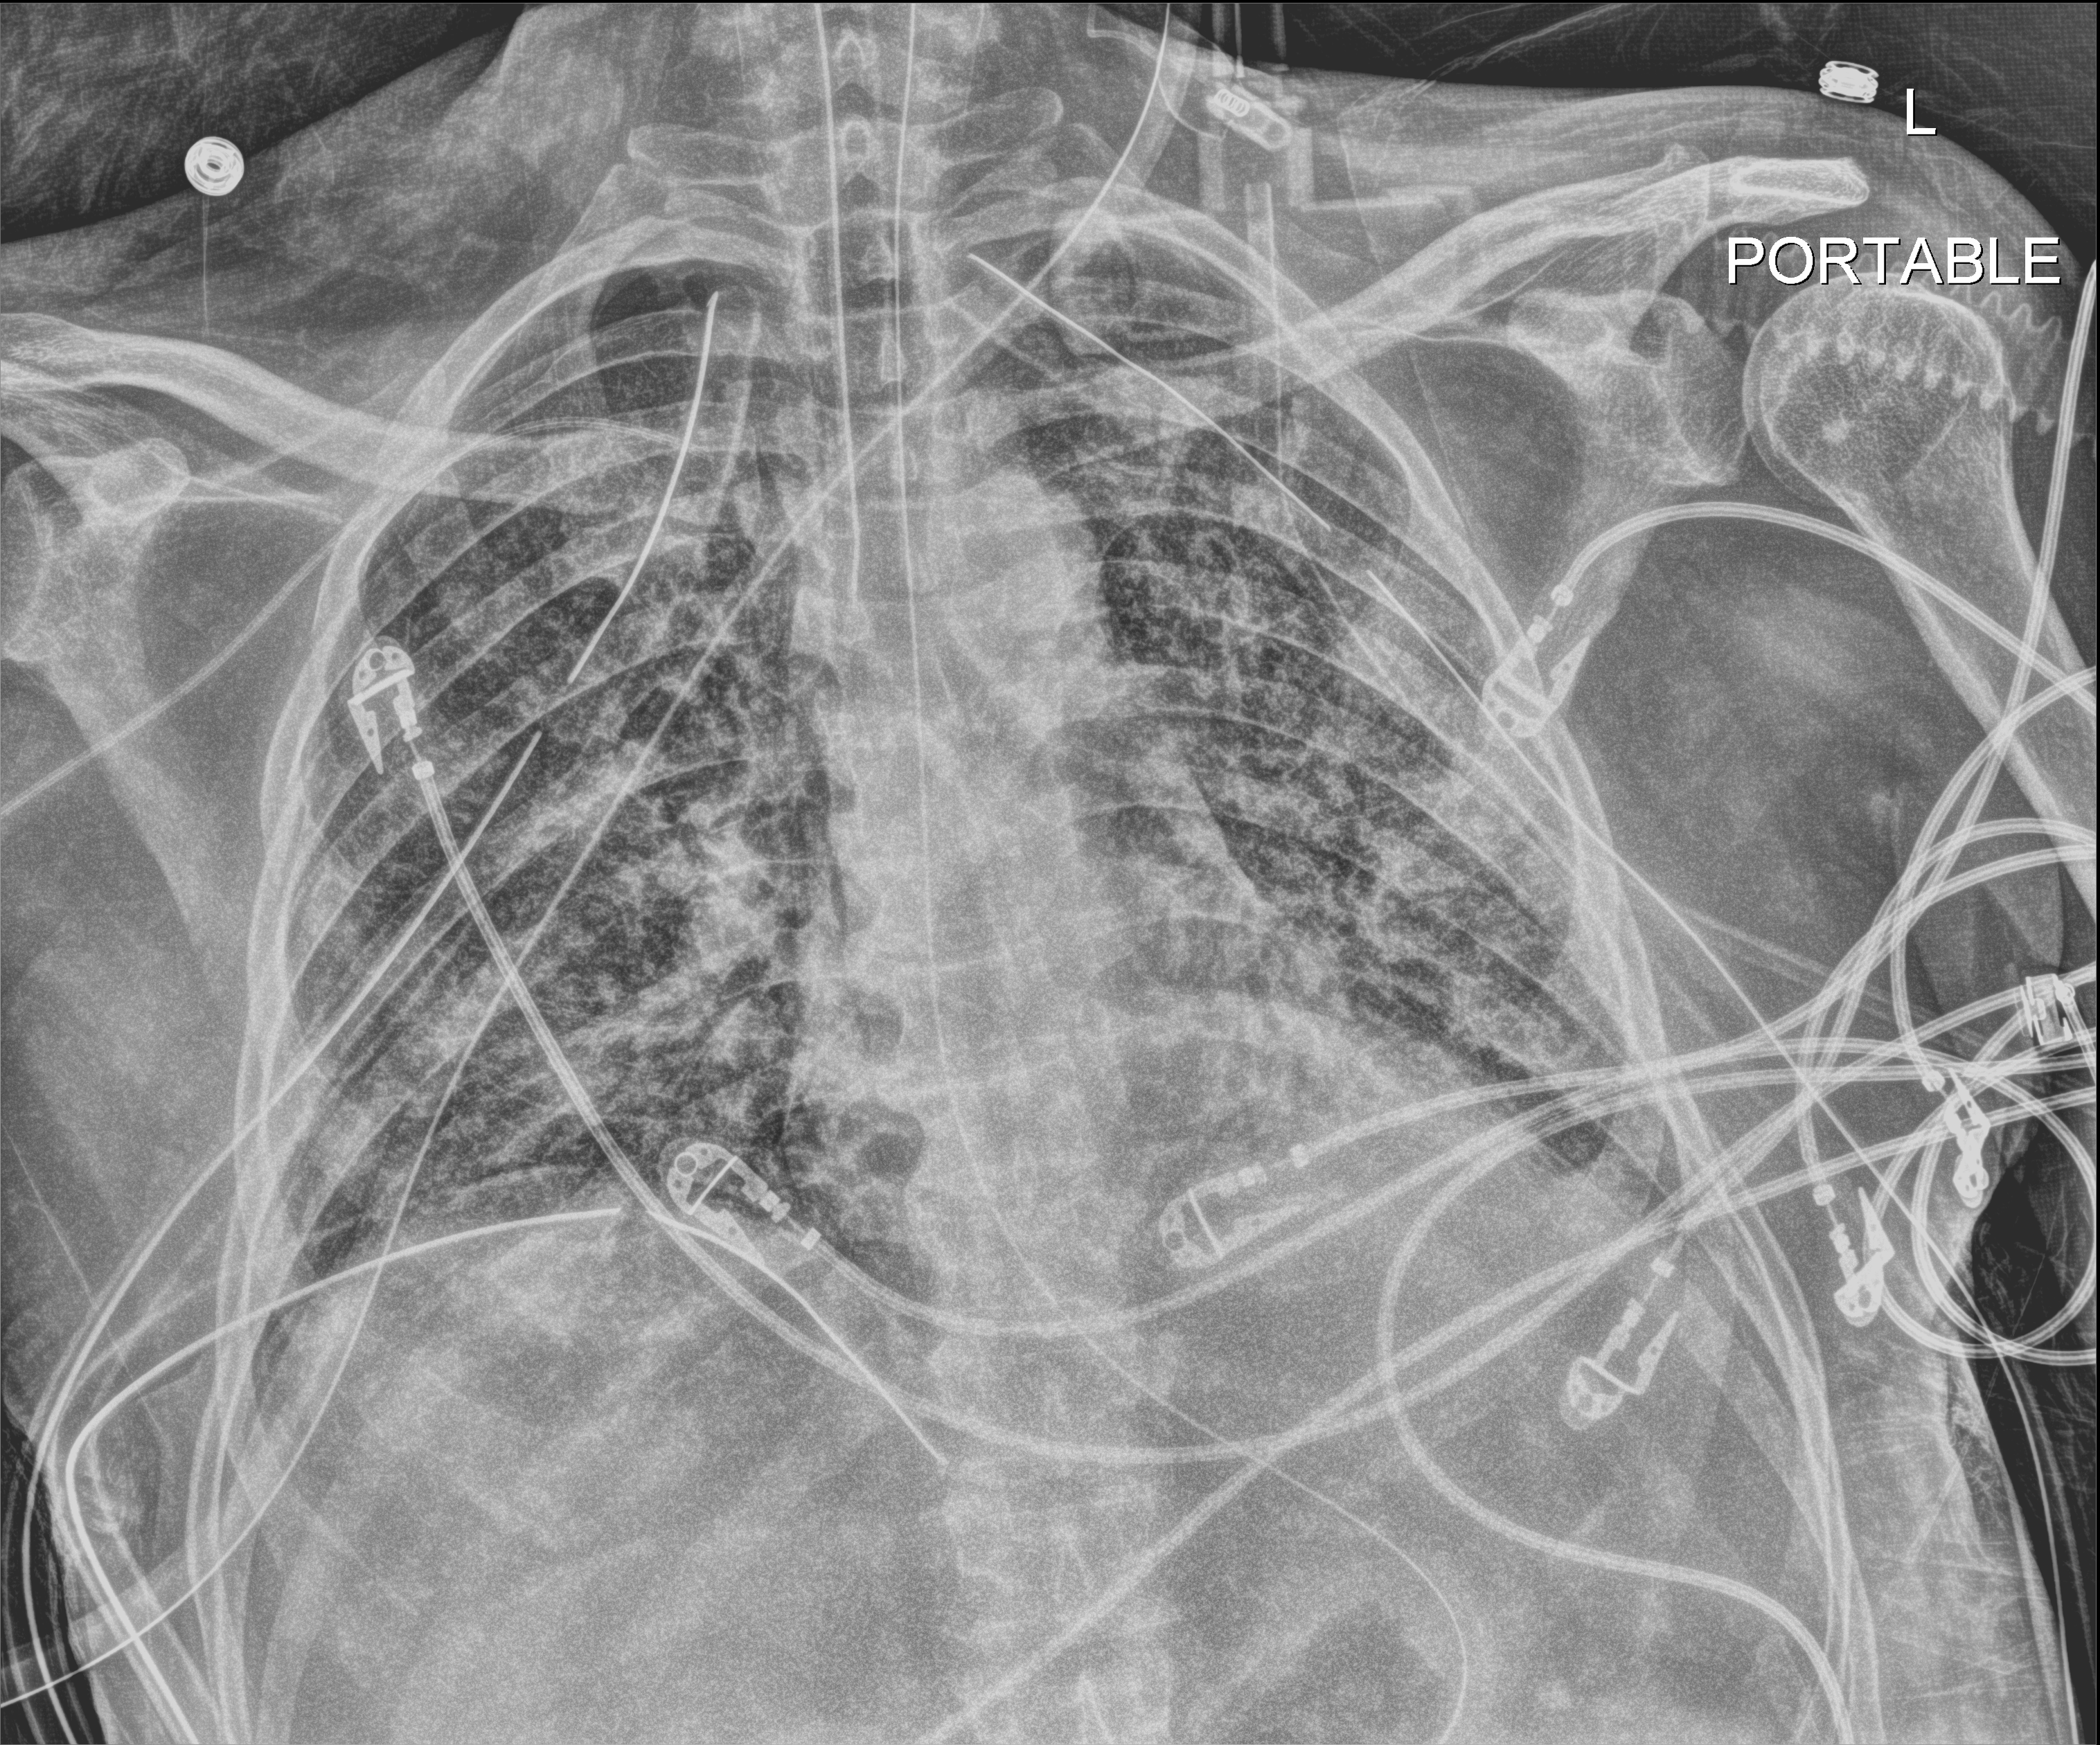
Bedside chest radiograph (digital radiography), anteroposterior (AP) projection. Patient hospitalised with COVID-19; male, aged 18–59 years.
From the hospital-stay record, not from the radiograph (when in the stay this image was taken is not recorded): chronic kidney disease (admission record): no; mechanically ventilated during this hospital stay: yes; admitted to intensive care during this hospital stay: yes.